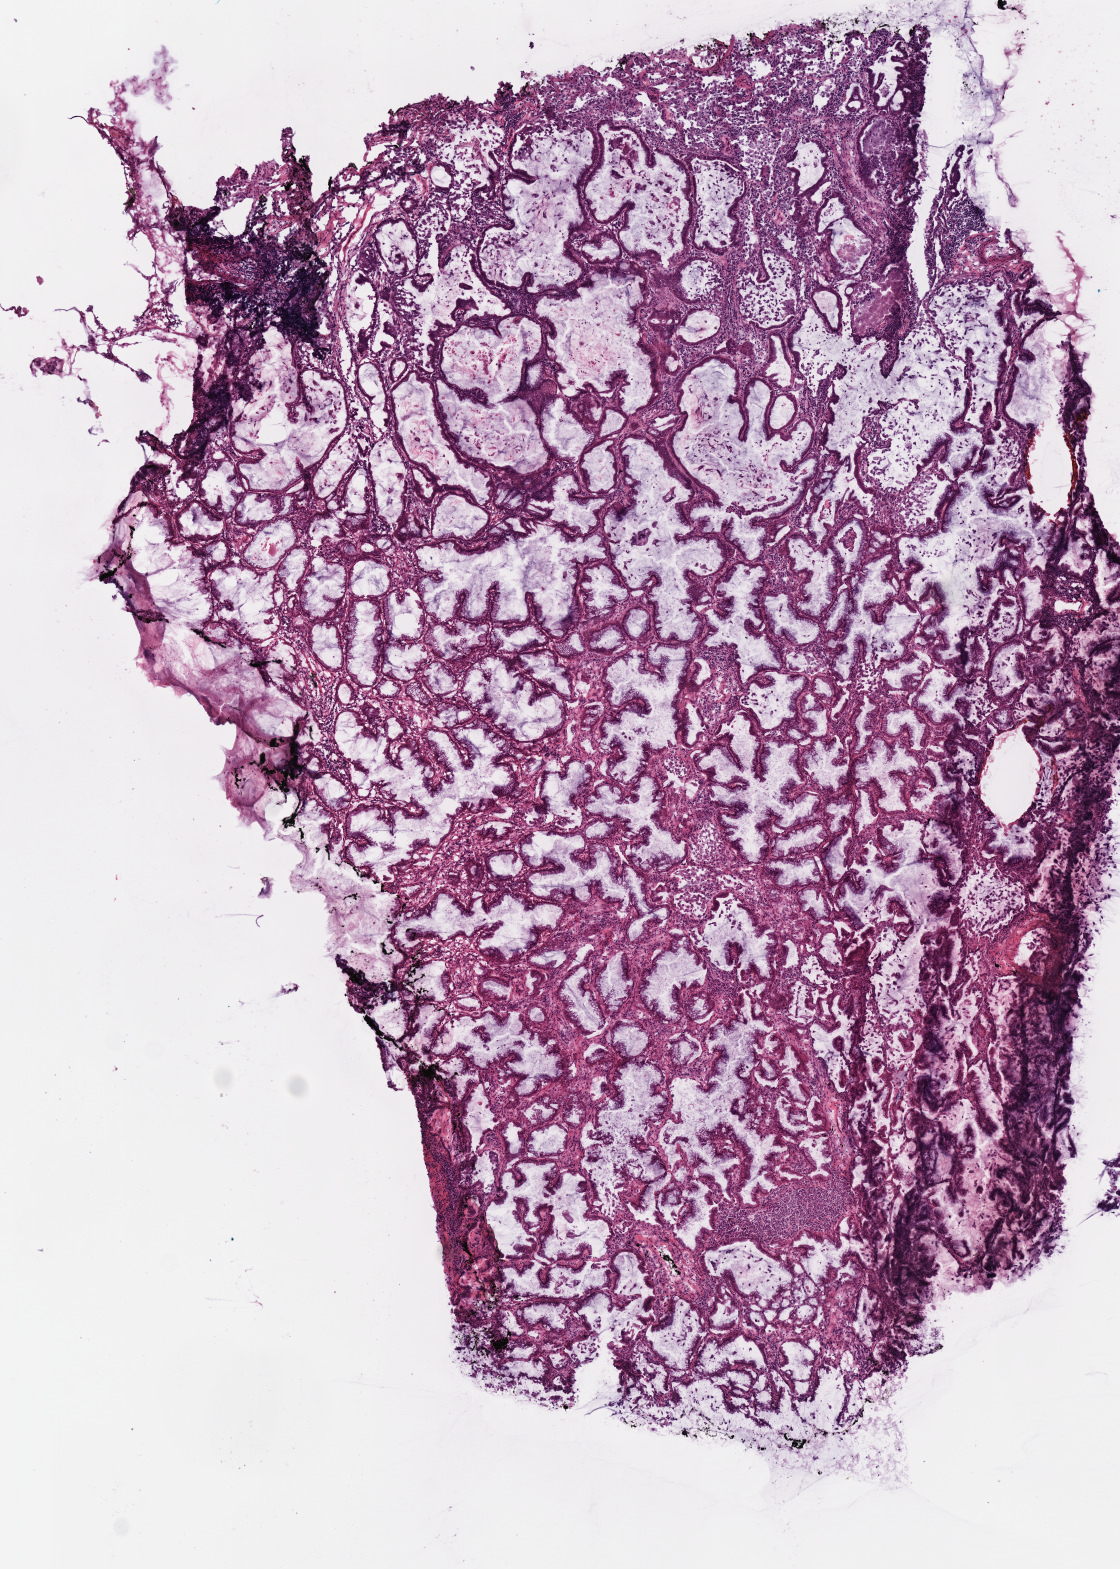
Digitized H&E-stained tissue section (whole slide) — a low-resolution overview of the entire scanned area, about 4.4 x 6.2 mm. Frozen section from the top of the tissue portion. Lung, primary tumour sample. Female patient; age at initial diagnosis 64 years. Slide review estimates, as recorded: tumour cells 85%, tumour nuclei 70%, normal cells 0%, stromal cells 15%, necrosis 0%.
Histologic diagnosis: Mucinous adenocarcinoma (upper lobe, lung). AJCC pathologic stage: IB (7th edition).